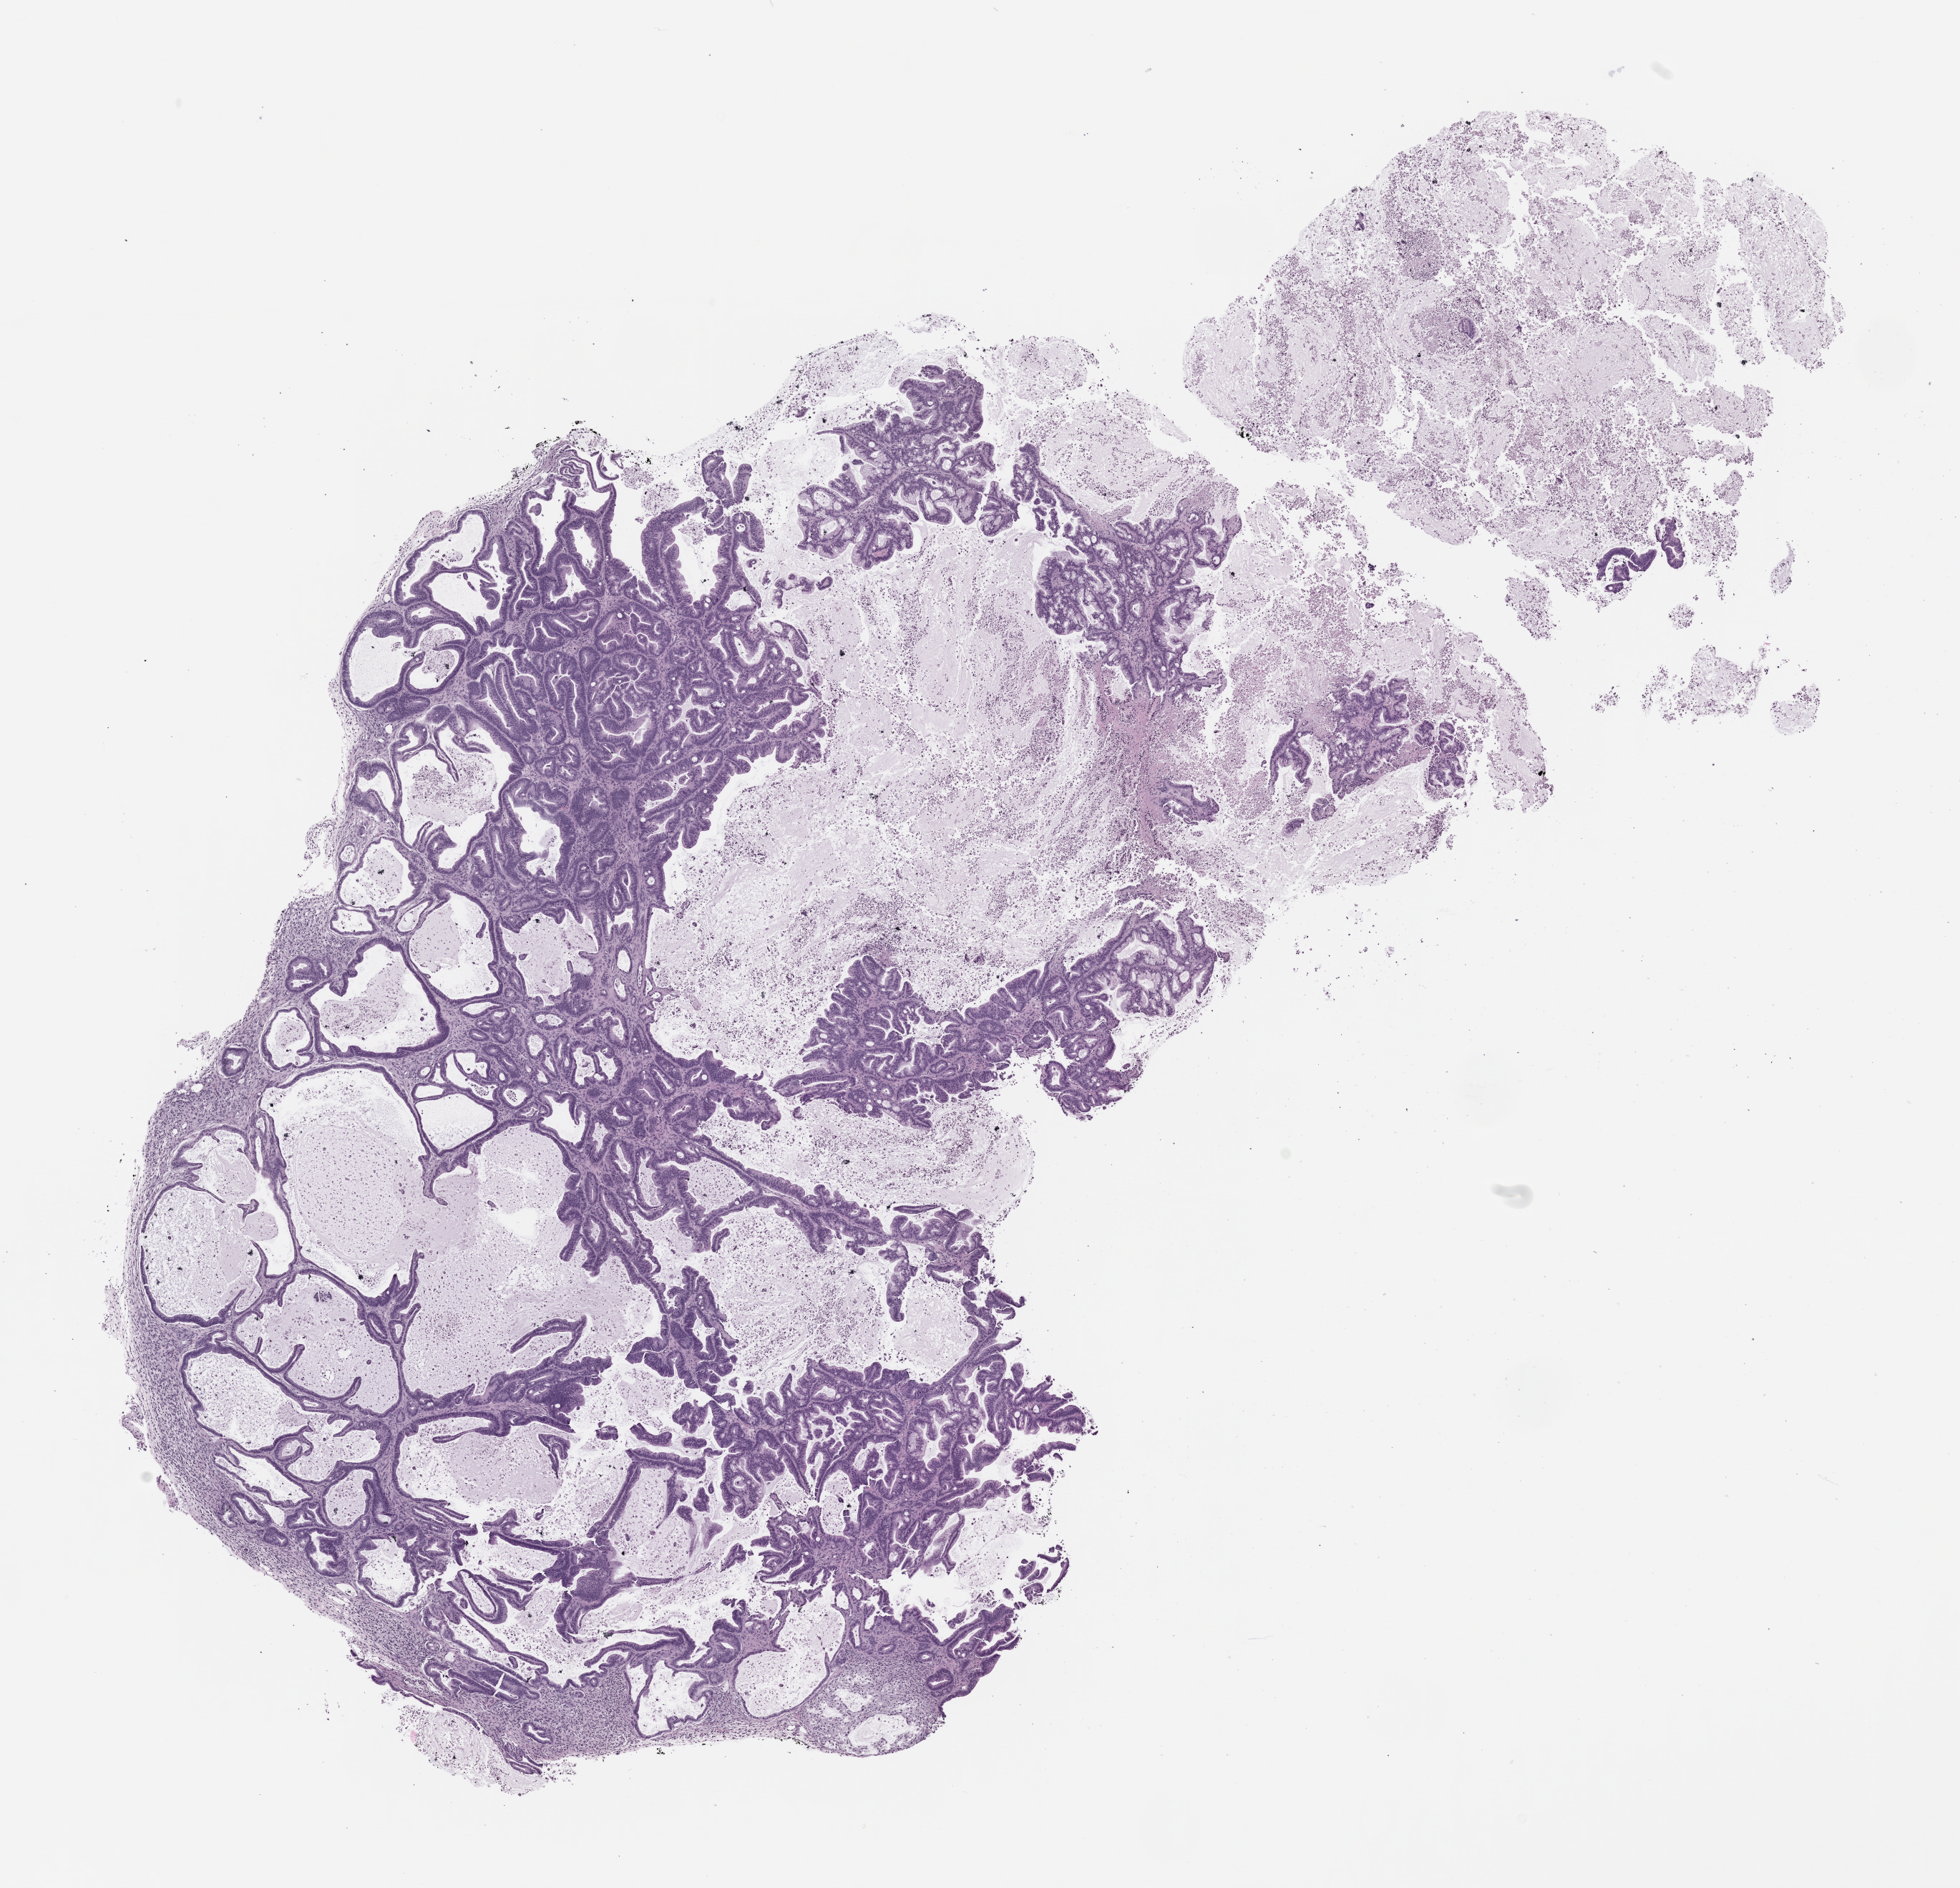
Whole-slide image, H&E: patient-derived xenograft (human tumor grown in a mouse), passage 2 — a low-resolution overview of the entire scanned area, about 11.0 x 10.6 mm; FFPE section; tumor site category: pancreas.
• originating patient diagnosis: Pancreatic Adenocarcinoma